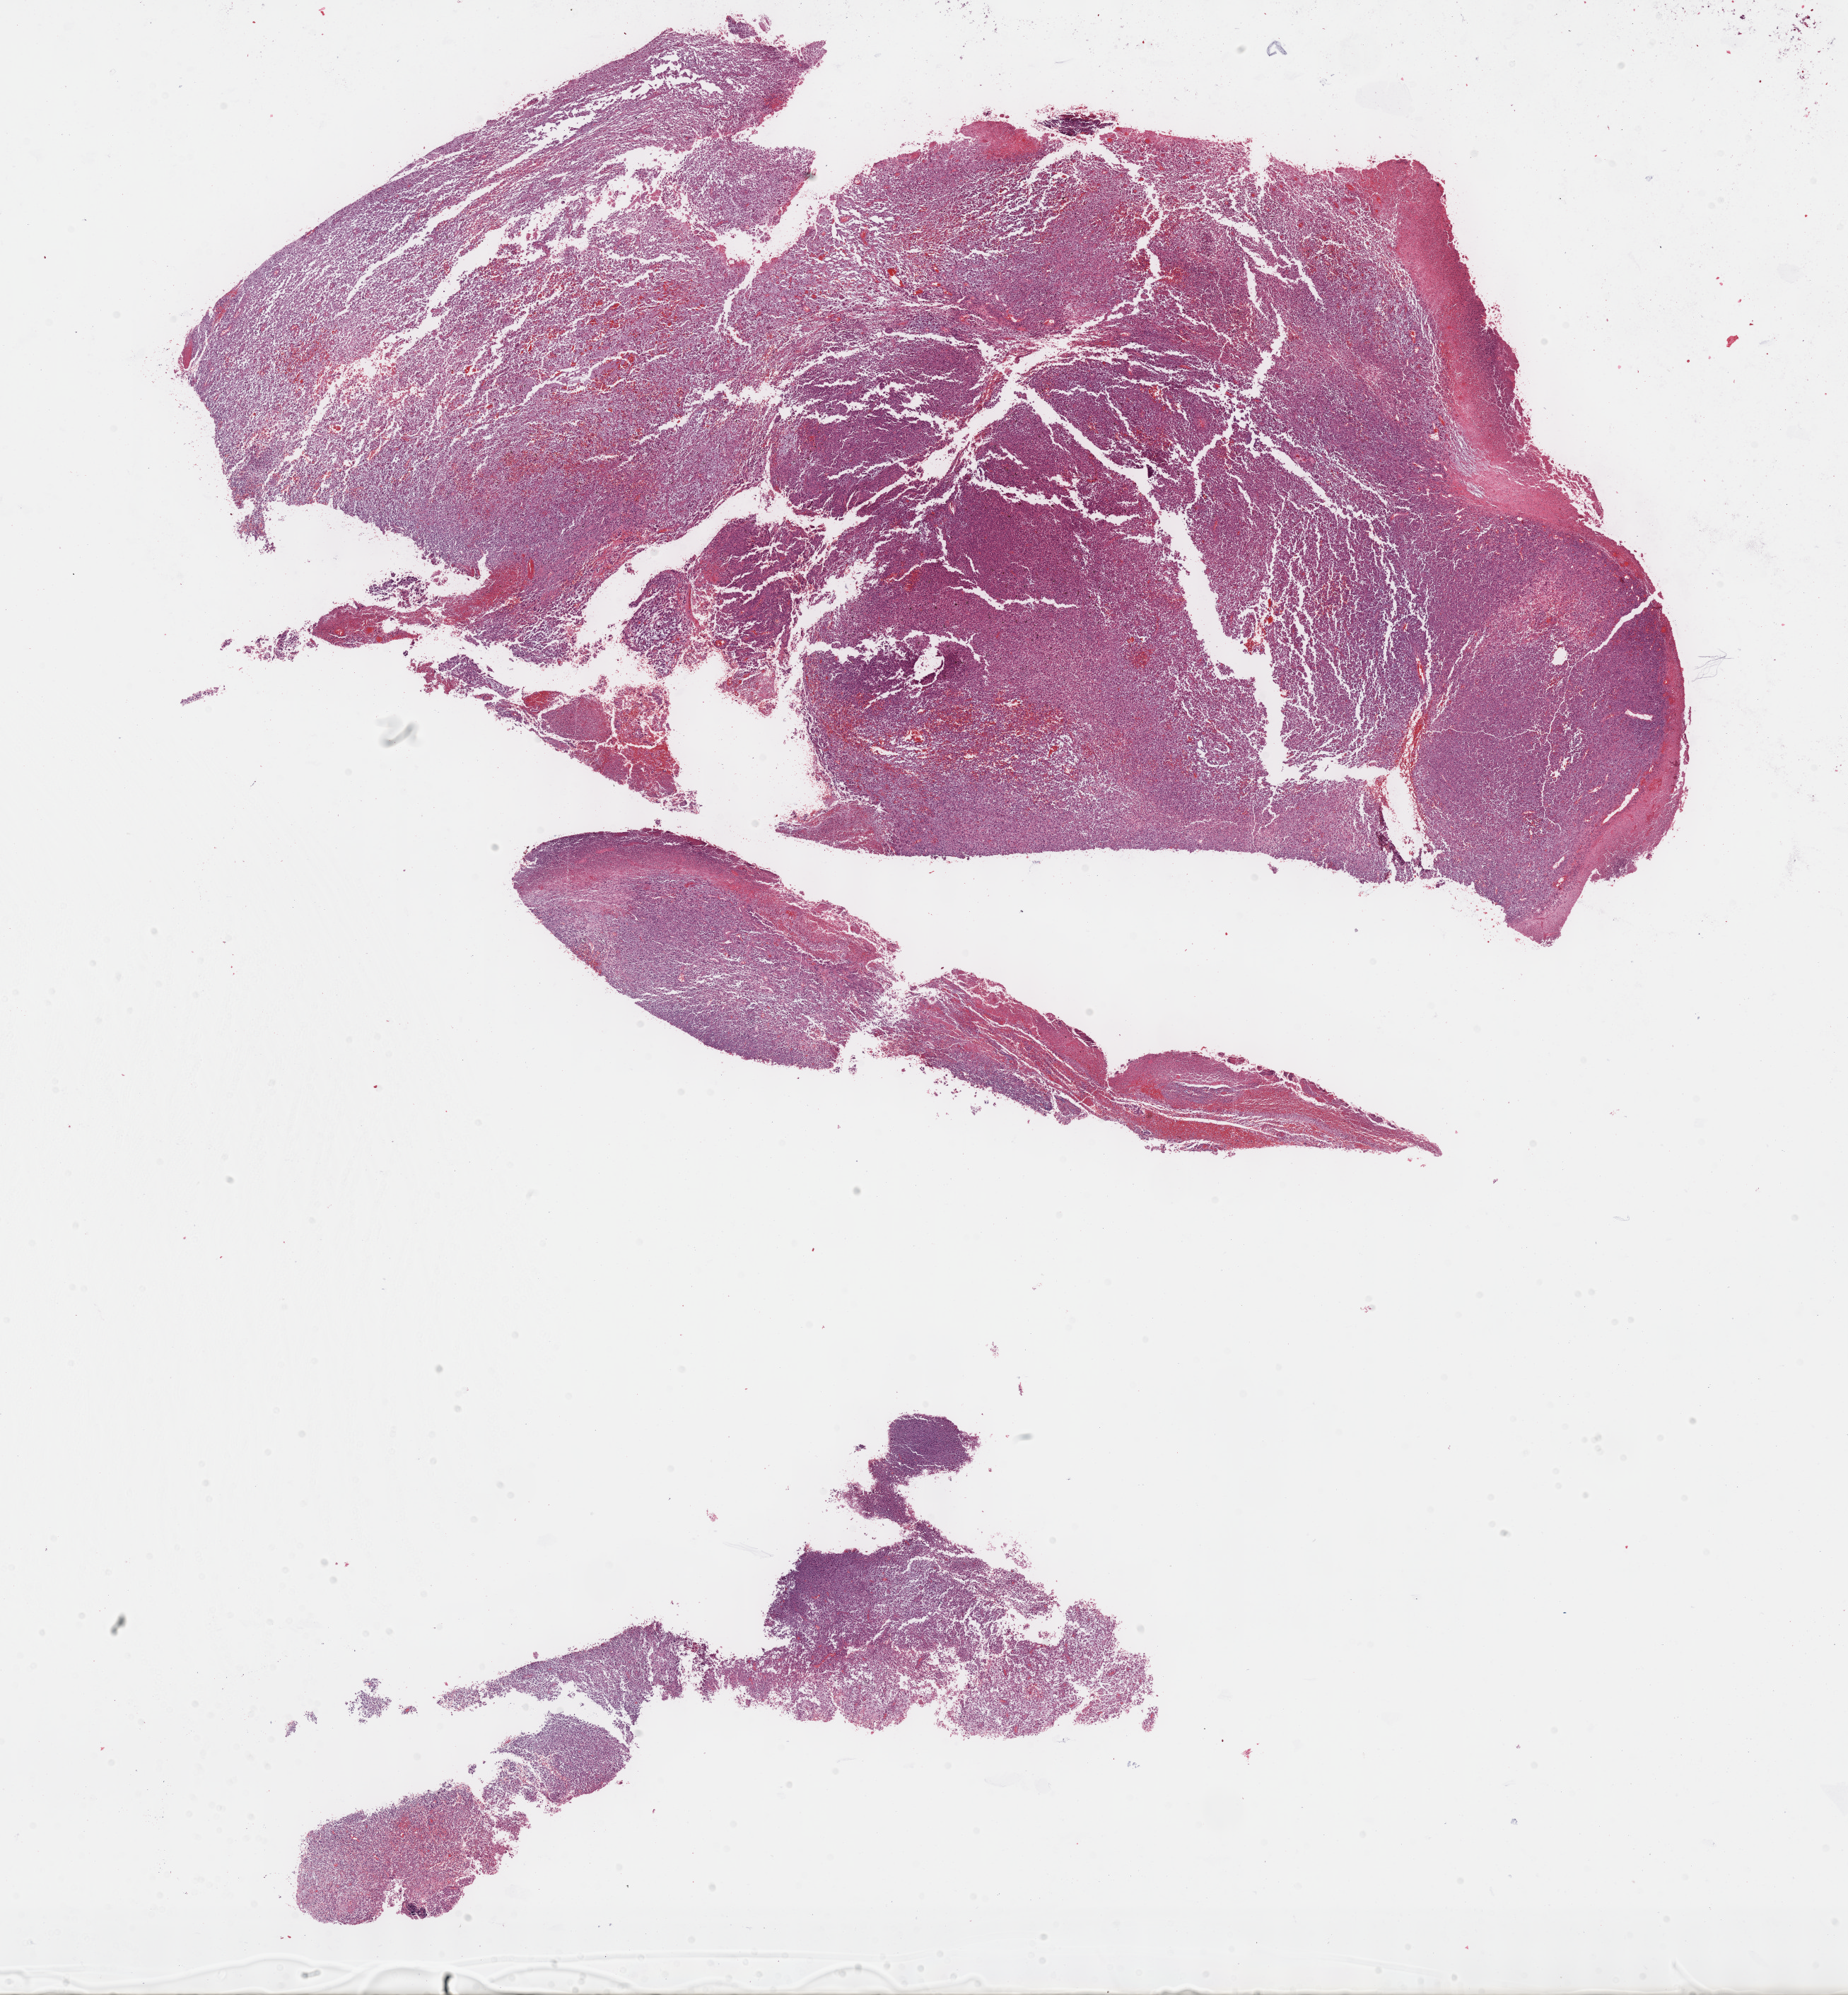
H&E whole-slide image — whole scanned area (about 21.1 x 22.8 mm, slide scanned at 40x) shown as a low-resolution overview; formalin-fixed paraffin-embedded (FFPE) diagnostic section; bladder, primary tumour sample. Male, age 81 years at initial diagnosis. Histologic grade: high grade.
Lymph nodes positive (case pathology): 0 of 111 examined. AJCC pathologic stage: II (6th edition). Histologic diagnosis: Papillary transitional cell carcinoma.